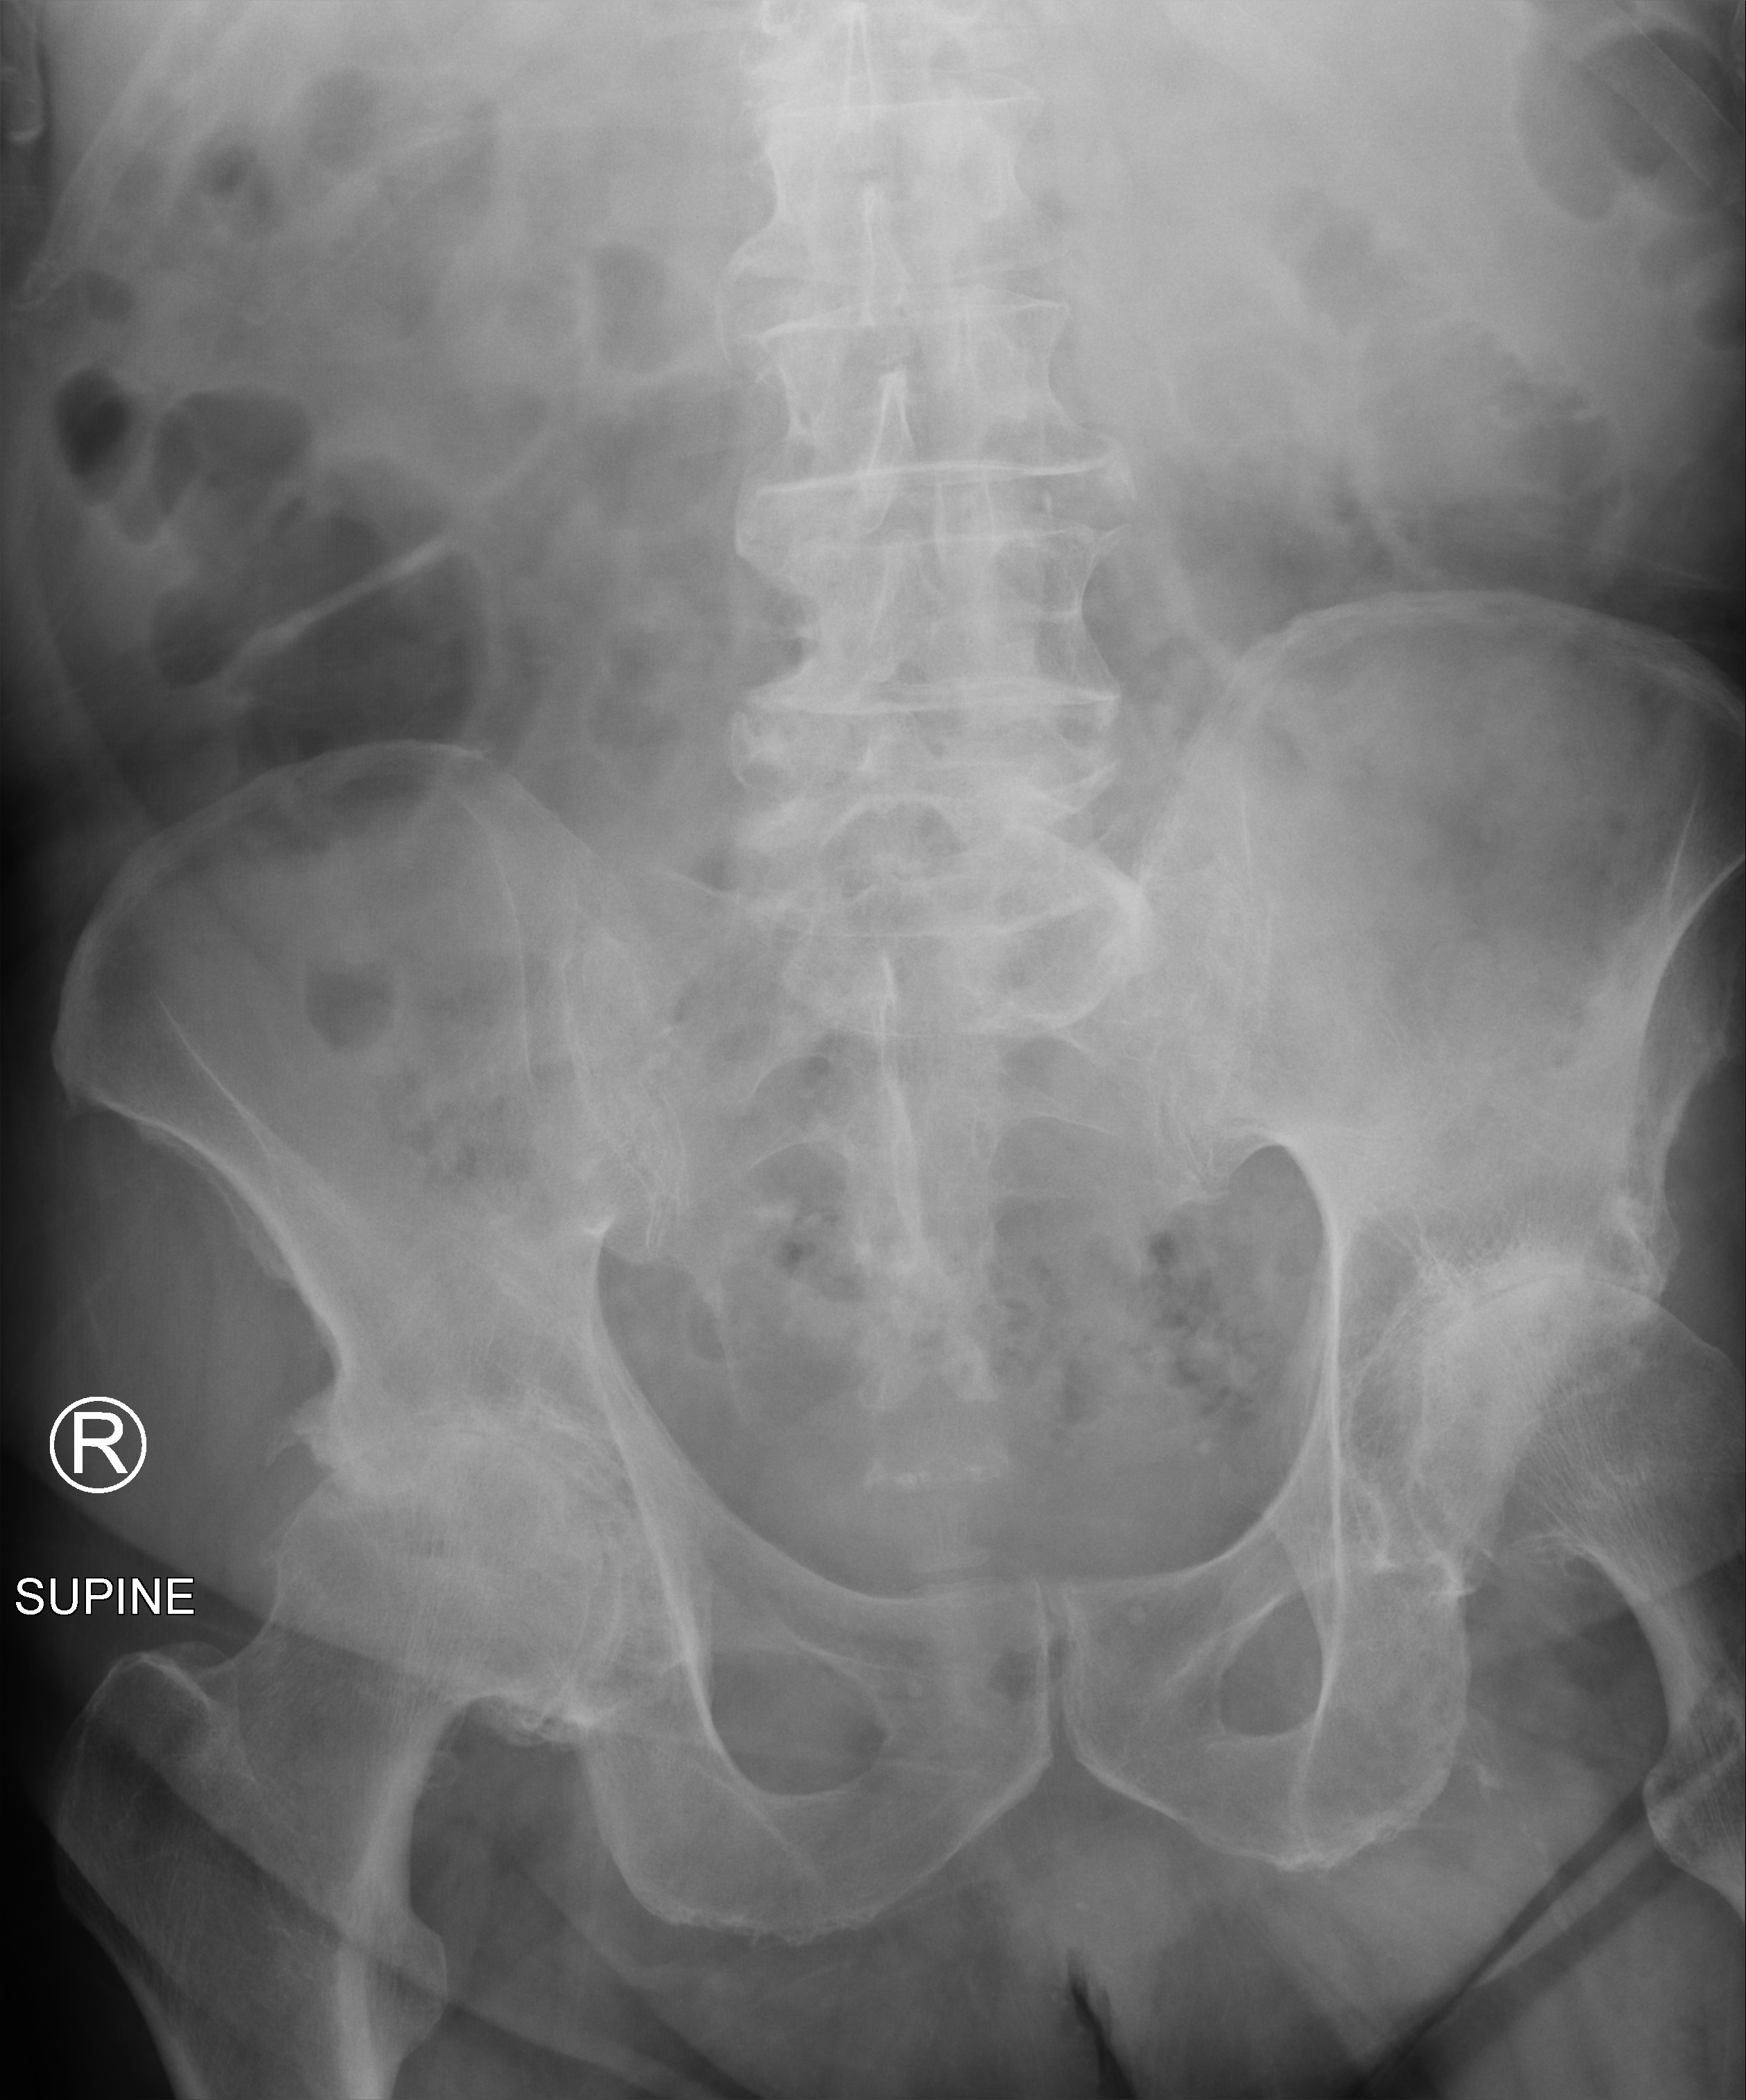
Bedside abdomen radiograph (computed radiography); anteroposterior (AP) projection. Male patient hospitalised with COVID-19, age 75–90 years.
Admission-level facts for this patient (not findings on this image; timing relative to this image not recorded): mechanically ventilated during this hospital stay: no.